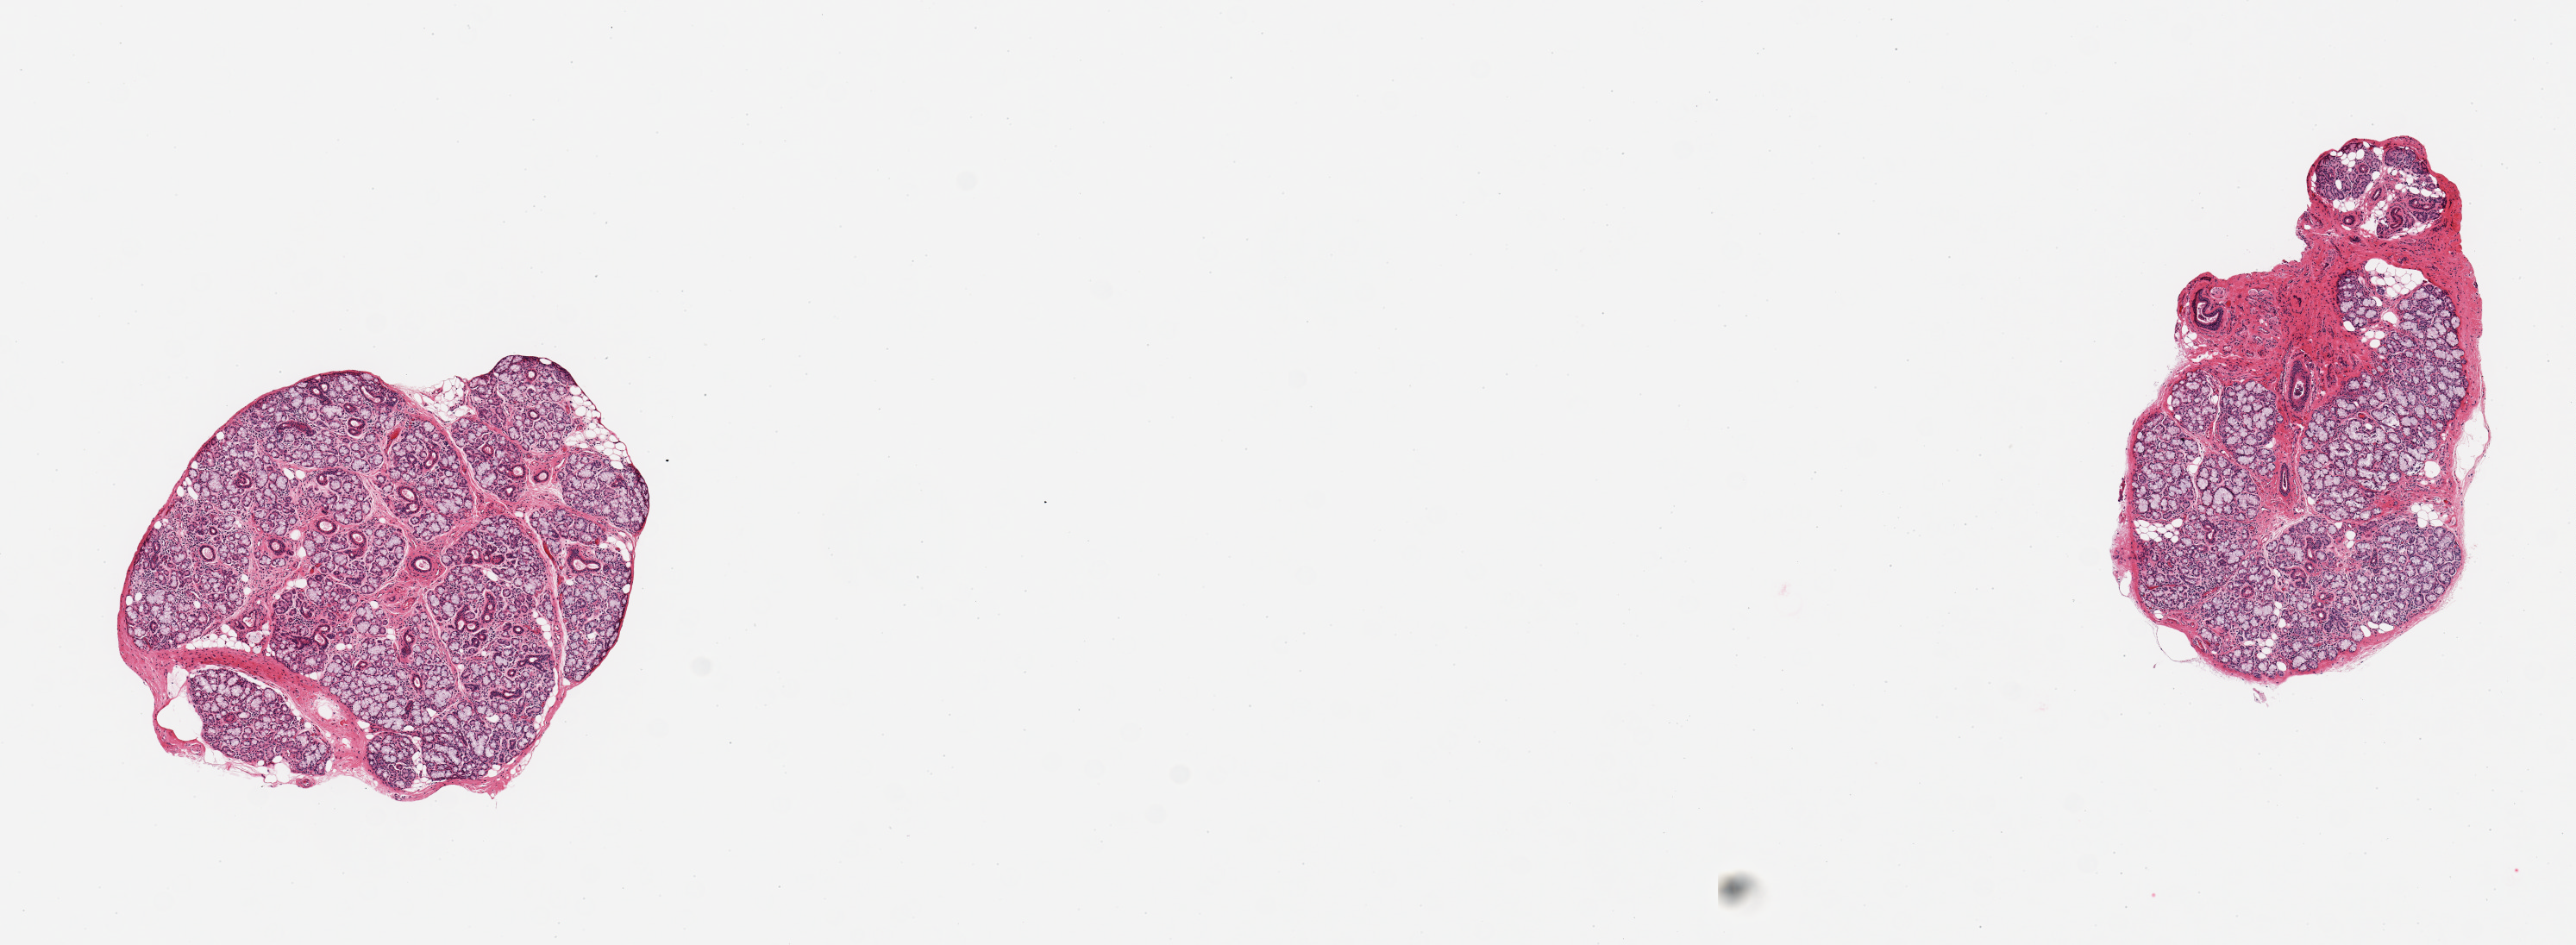
Haematoxylin and eosin whole-slide image, whole scanned area (about 11.8 x 4.3 mm) shown as a low-resolution overview. PAXgene-fixed paraffin-embedded (PFPE) section. Section of minor salivary gland (target tissue). Donor tissue sample. Male donor.
Pathologist's review note for this sample: 2 pieces, ~90% glandular elements.